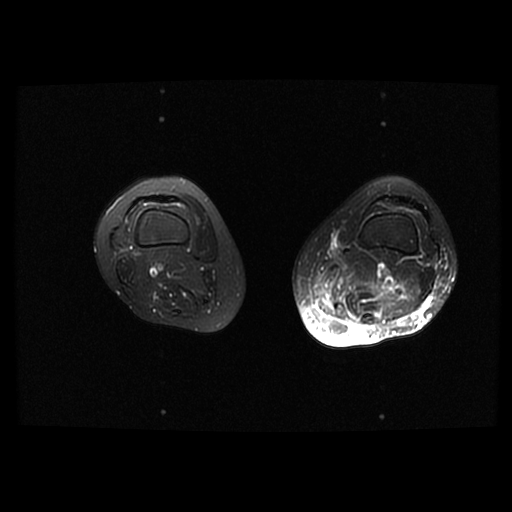
MRI of an extremity soft-tissue mass, one axial slice; slice 14 of 42 in the series (ordered by position); T2-weighted fat-saturated; 6 mm slice thickness; 512 × 512 image matrix, field of view 420 × 420 mm. Female patient. Case-level facts recorded for this patient, not image findings: histological type: pleomorphic leiomyosarcoma; grade: high; site of the primary tumour: left thigh.
Structures marked on this image (outlined manually by an expert reader):
- gross tumour volume including surrounding oedema: bounding box [x1, y1, x2, y2] px = [313, 264, 346, 318]